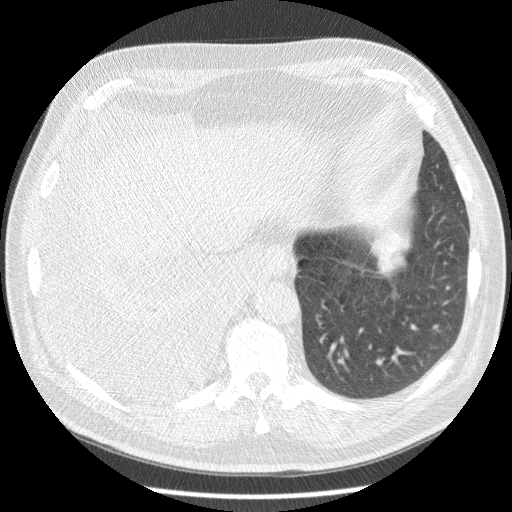
Low-dose screening chest CT, one axial slice. Slice 51 of 180 in the series (ordered by position). 120 kVp. Lung window (W 1500 / L -600 HU). 2.5 mm slice thickness. 512 × 512 image matrix.
Annotated regions visible in this slice (outlined manually by an expert reader):
- lesion 1 (tumor, lower lobe of left lung): bounding box [x1, y1, x2, y2] px = [371, 231, 408, 276]